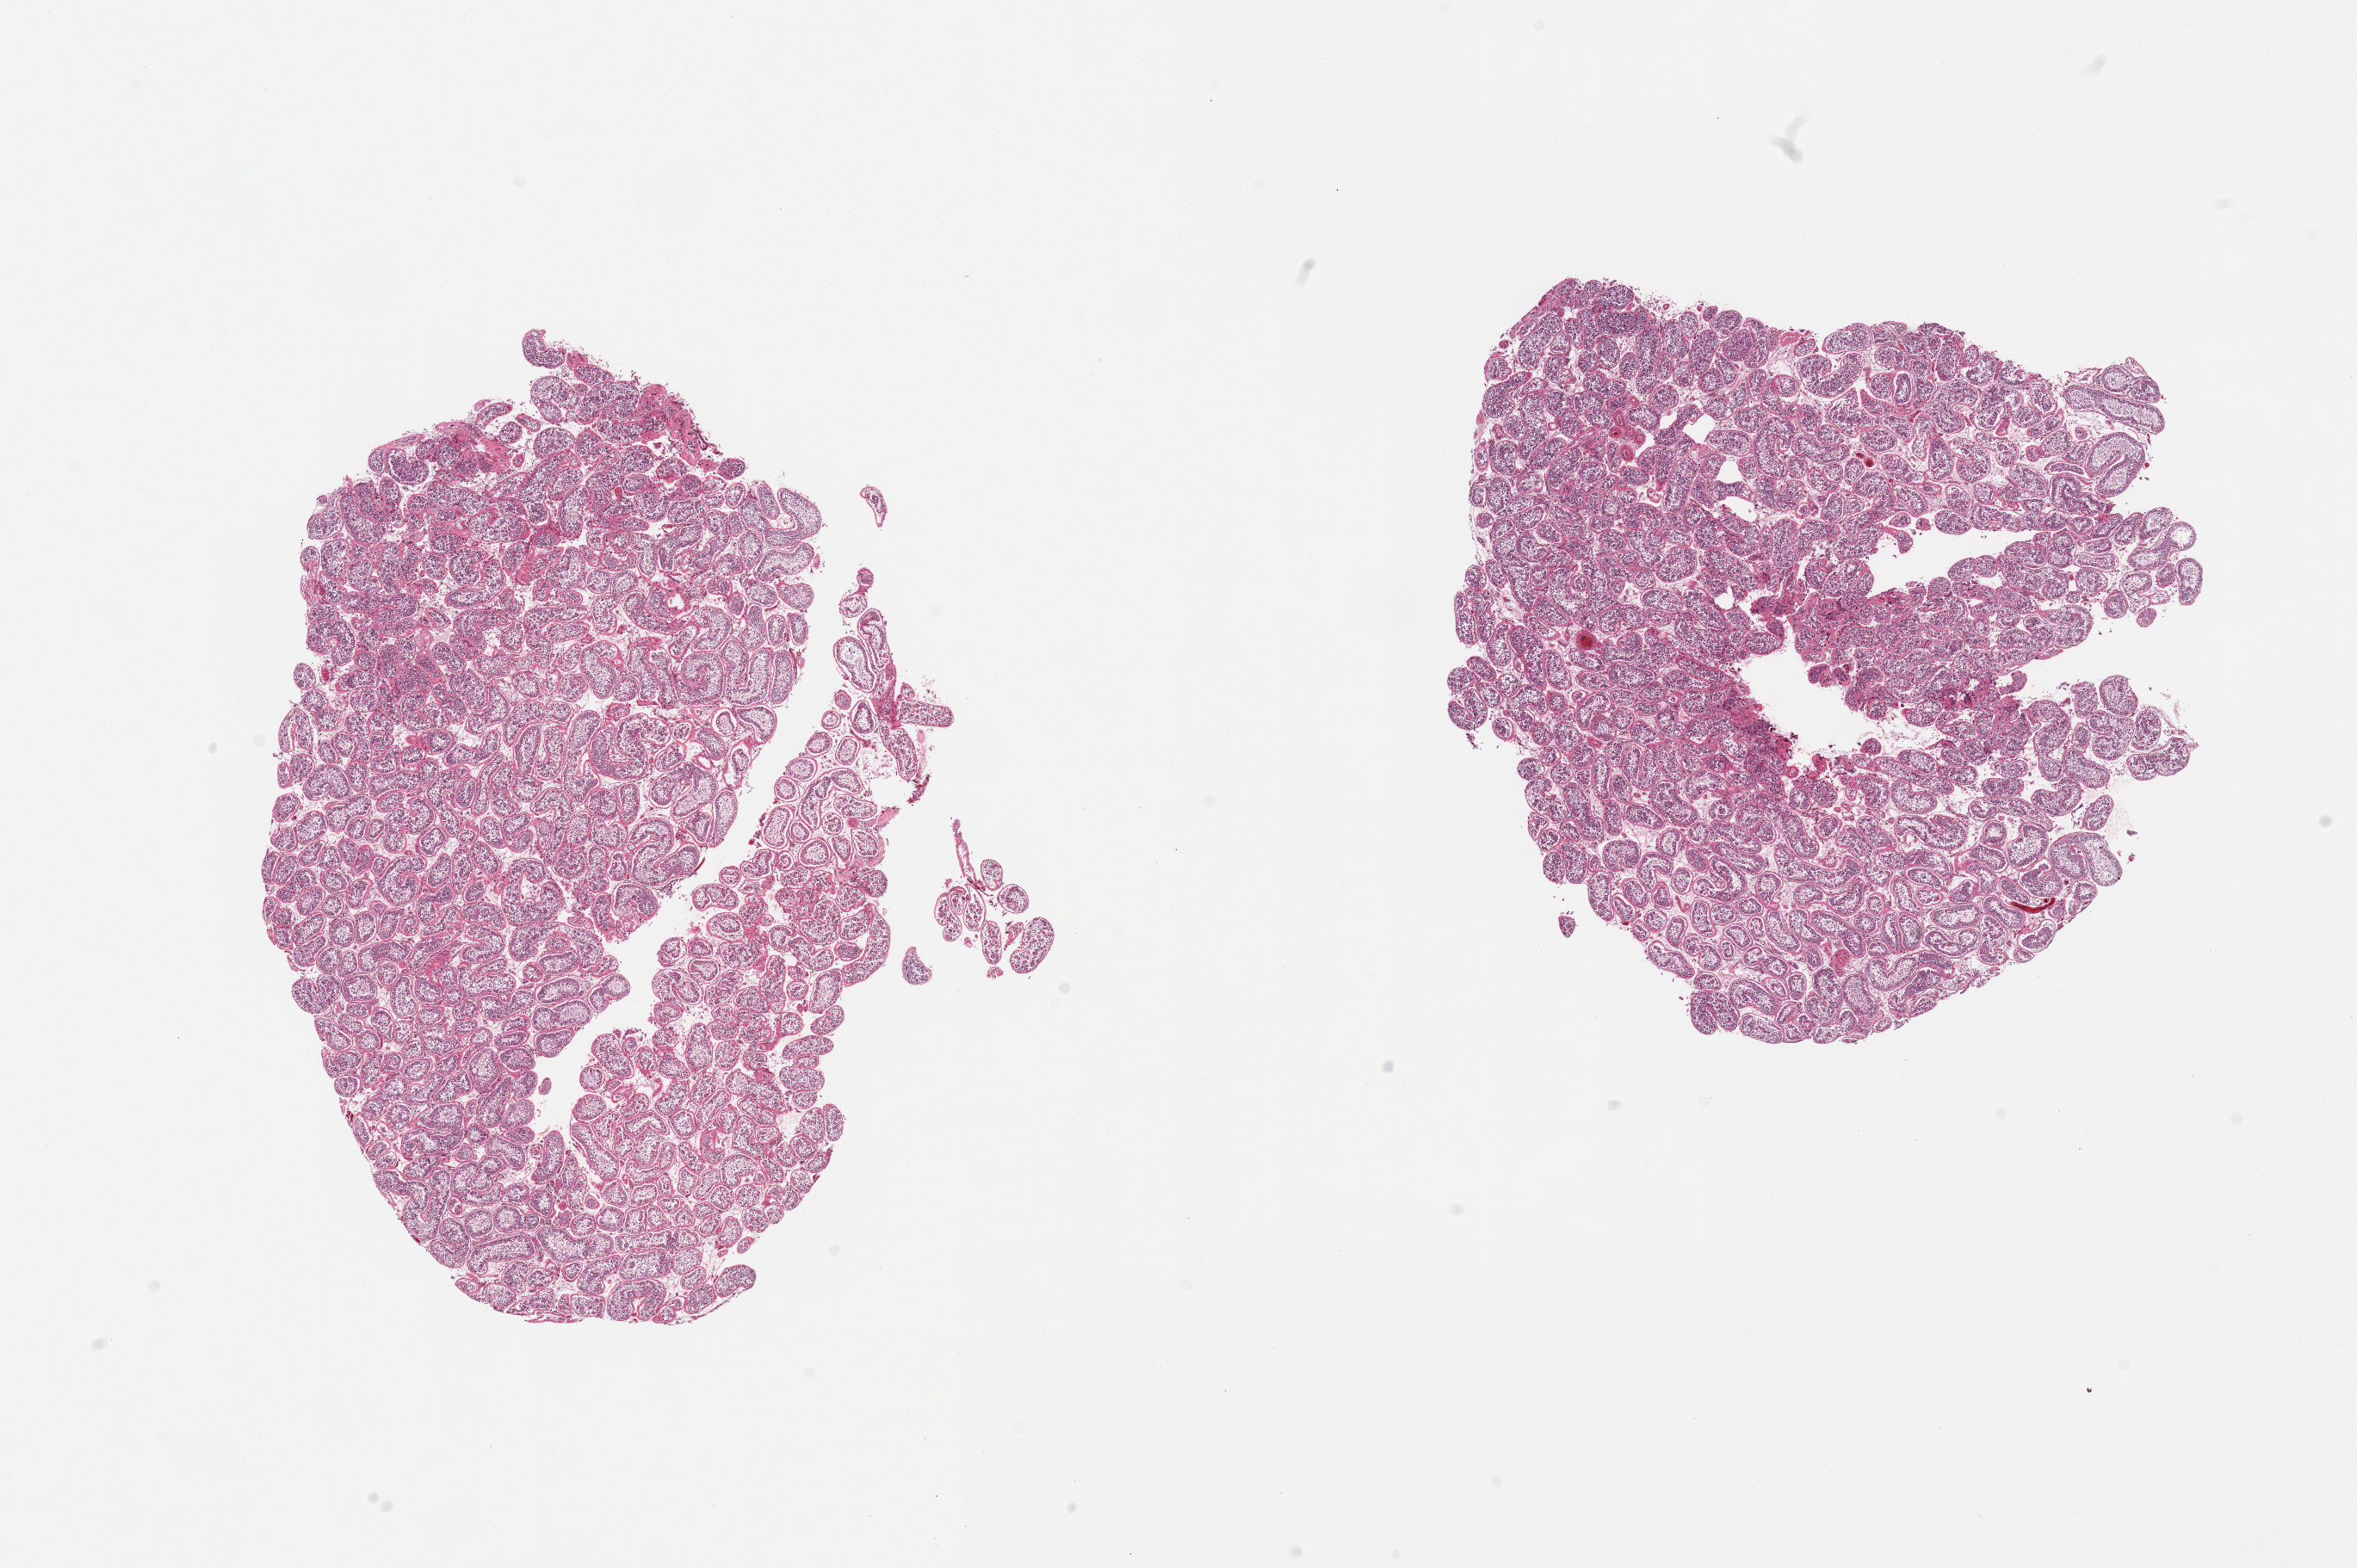
Digitized haematoxylin and eosin-stained section, whole scanned area (about 21.7 x 14.4 mm) shown as a low-resolution overview; PAXgene-fixed paraffin-embedded (PFPE) section; section of testis (target tissue); tissue donor sample.
Pathologist's review note for this sample: 2 pieces, tubular cells markedly autolyzed.